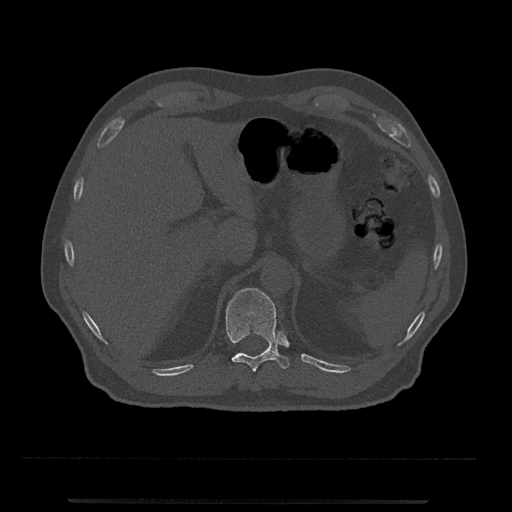
CT including the spine, one axial slice. Slice 462 of 797 in the series (ordered by position). 120 kVp. Bone window (W 1800 / L 400 HU). 512 × 512 image matrix. Male patient, age 63 years. Case-level facts recorded for this patient, not image findings: primary cancer: prostate.
Annotated regions visible in this slice (semi-automatic segmentation, software-assisted and operator-edited):
- T11 vertebra: box from (x=226, y=288) to (x=291, y=372) px